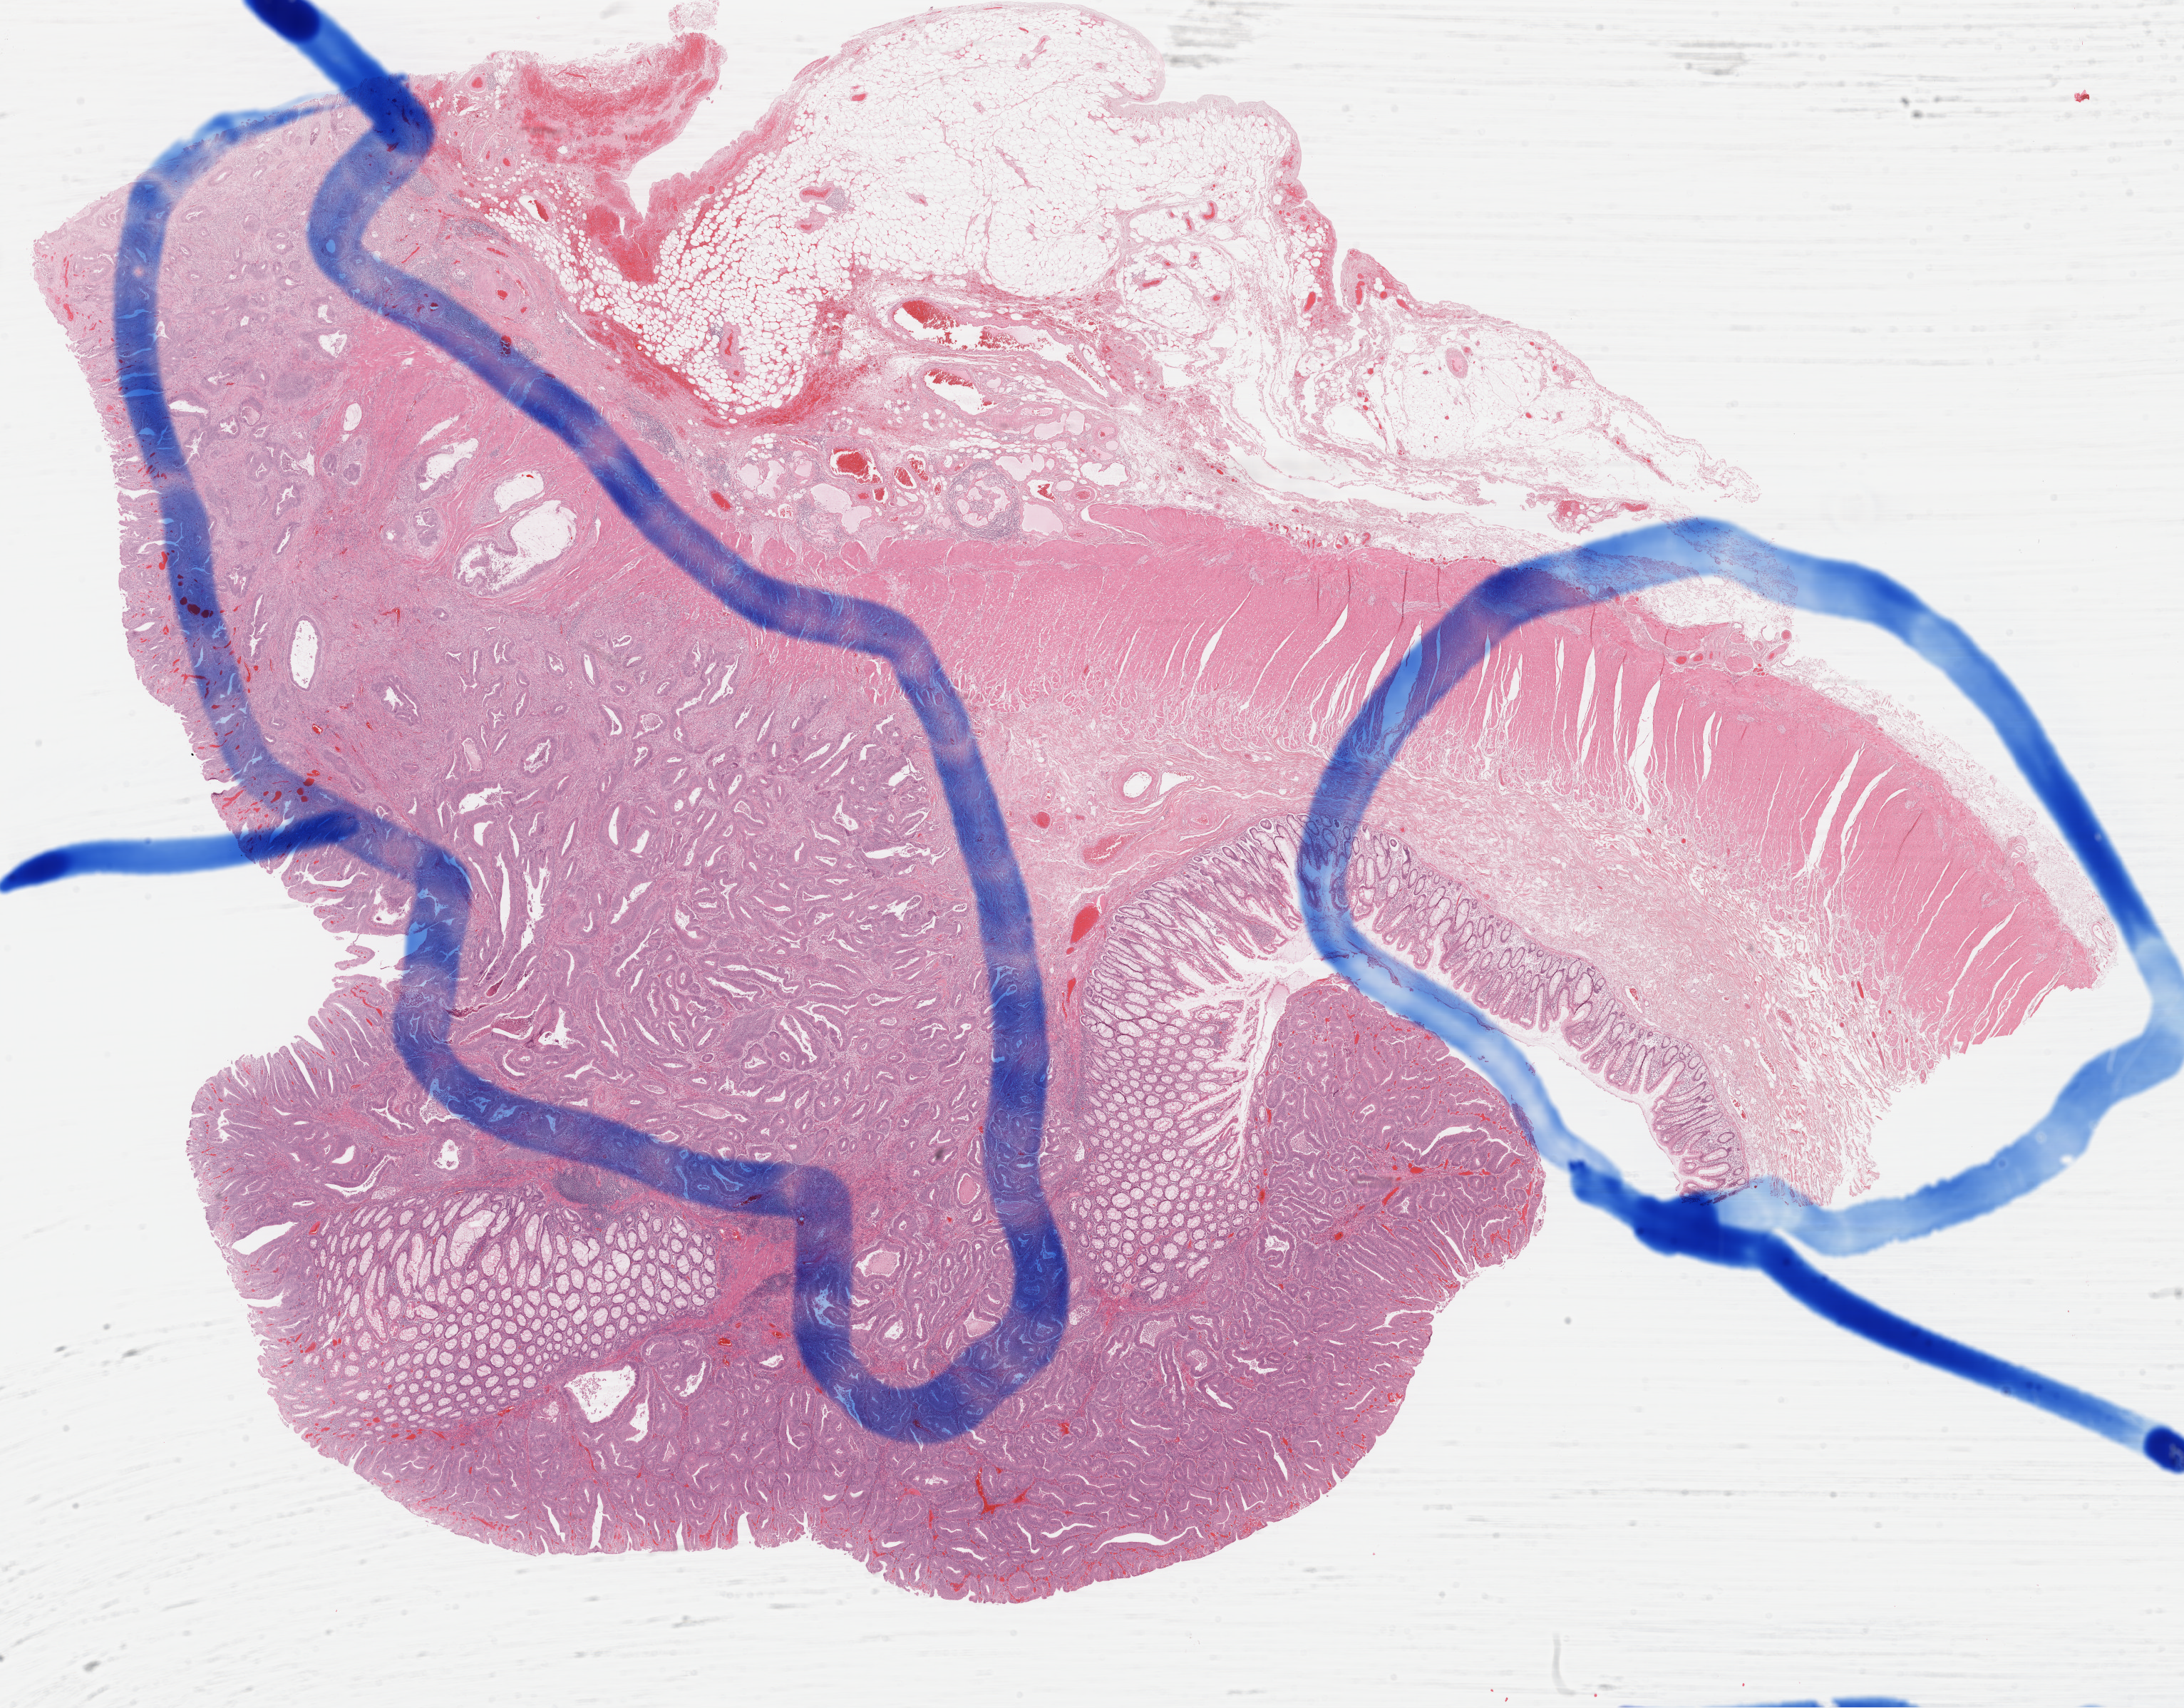
Whole-slide histology image, Hematoxylin and eosin (H&E) stained, a low-resolution overview of the entire scanned area, about 24.2 x 18.9 mm (slide scanned at 40x); formalin-fixed paraffin-embedded (FFPE) diagnostic section; primary tumour sample from the colon. Female, age 71 years at initial diagnosis.
Lymph nodes positive (case pathology): 0 of 16 examined. Diagnosis: Adenocarcinoma, NOS (ascending colon). AJCC pathologic stage: IIA.